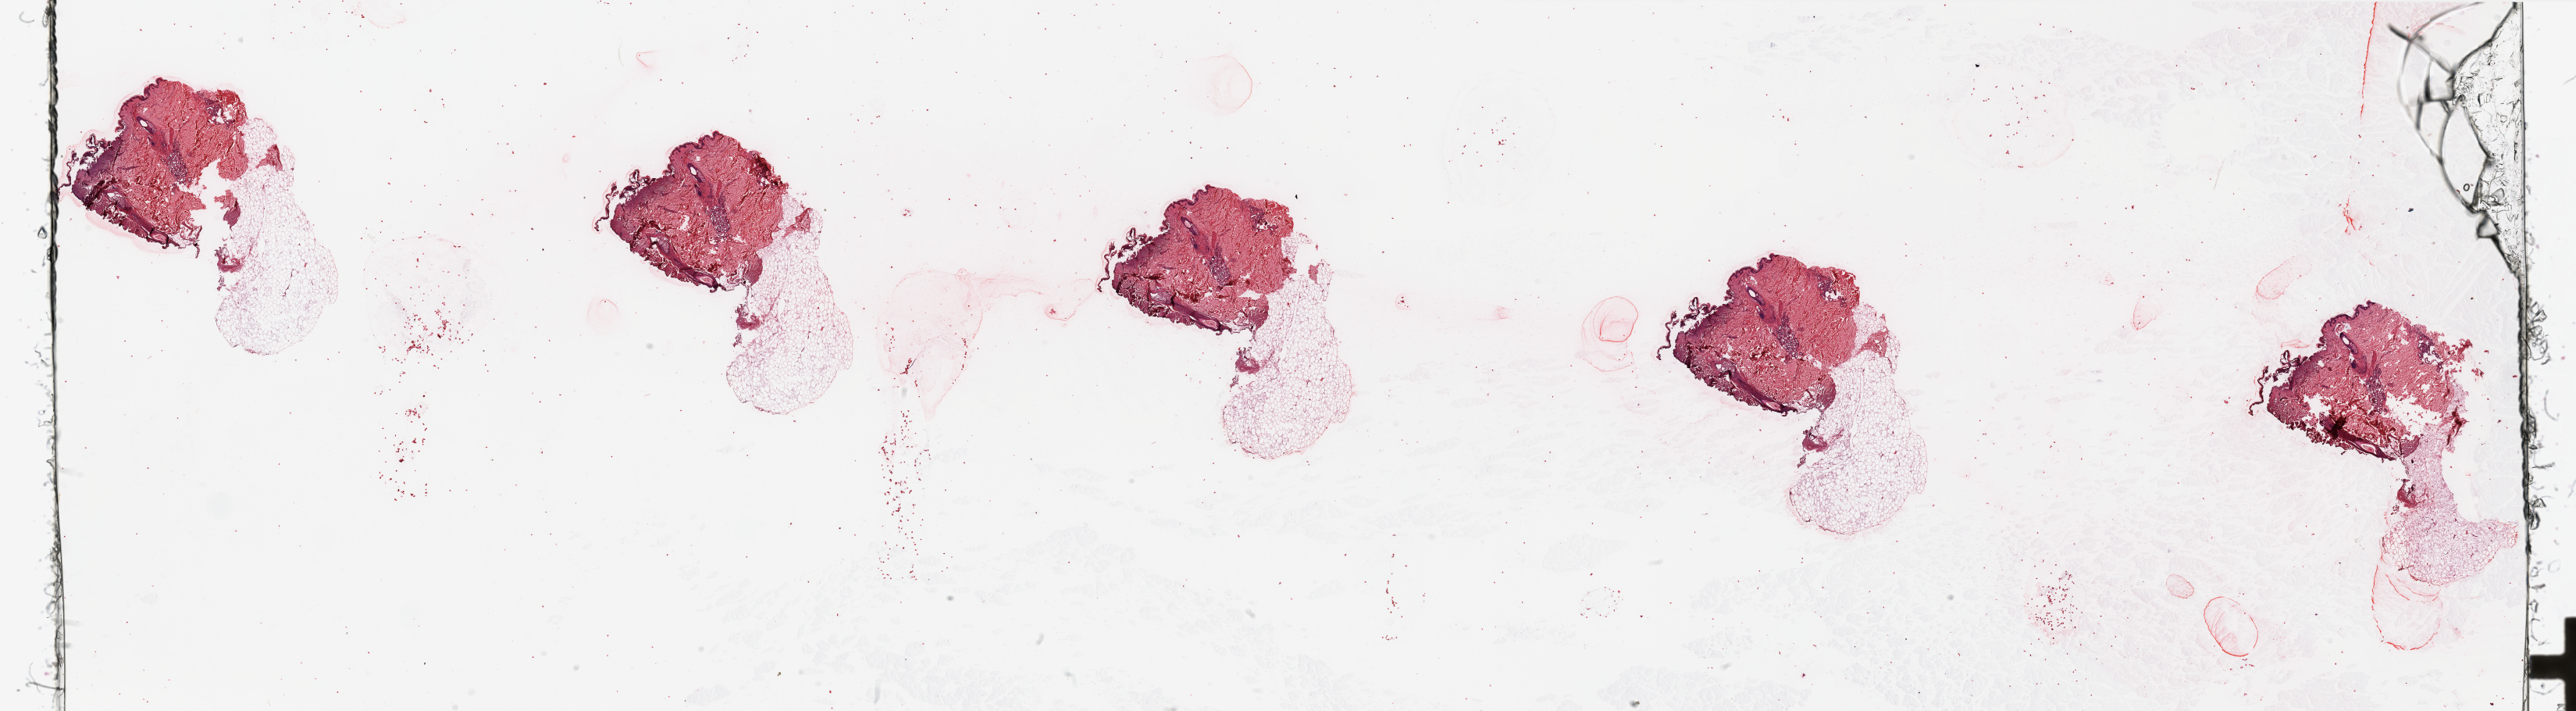
H&E whole-slide image, shown as a low-resolution overview of the whole scanned area (about 52.2 x 14.4 mm, slide scanned at 20x), normal (non-tumour) tissue sample, sampled site: trunk. Male, 69 y/o.
This section: normal (non-tumour) tissue from the same patient. Patient diagnosis: Malignant melanoma, NOS.